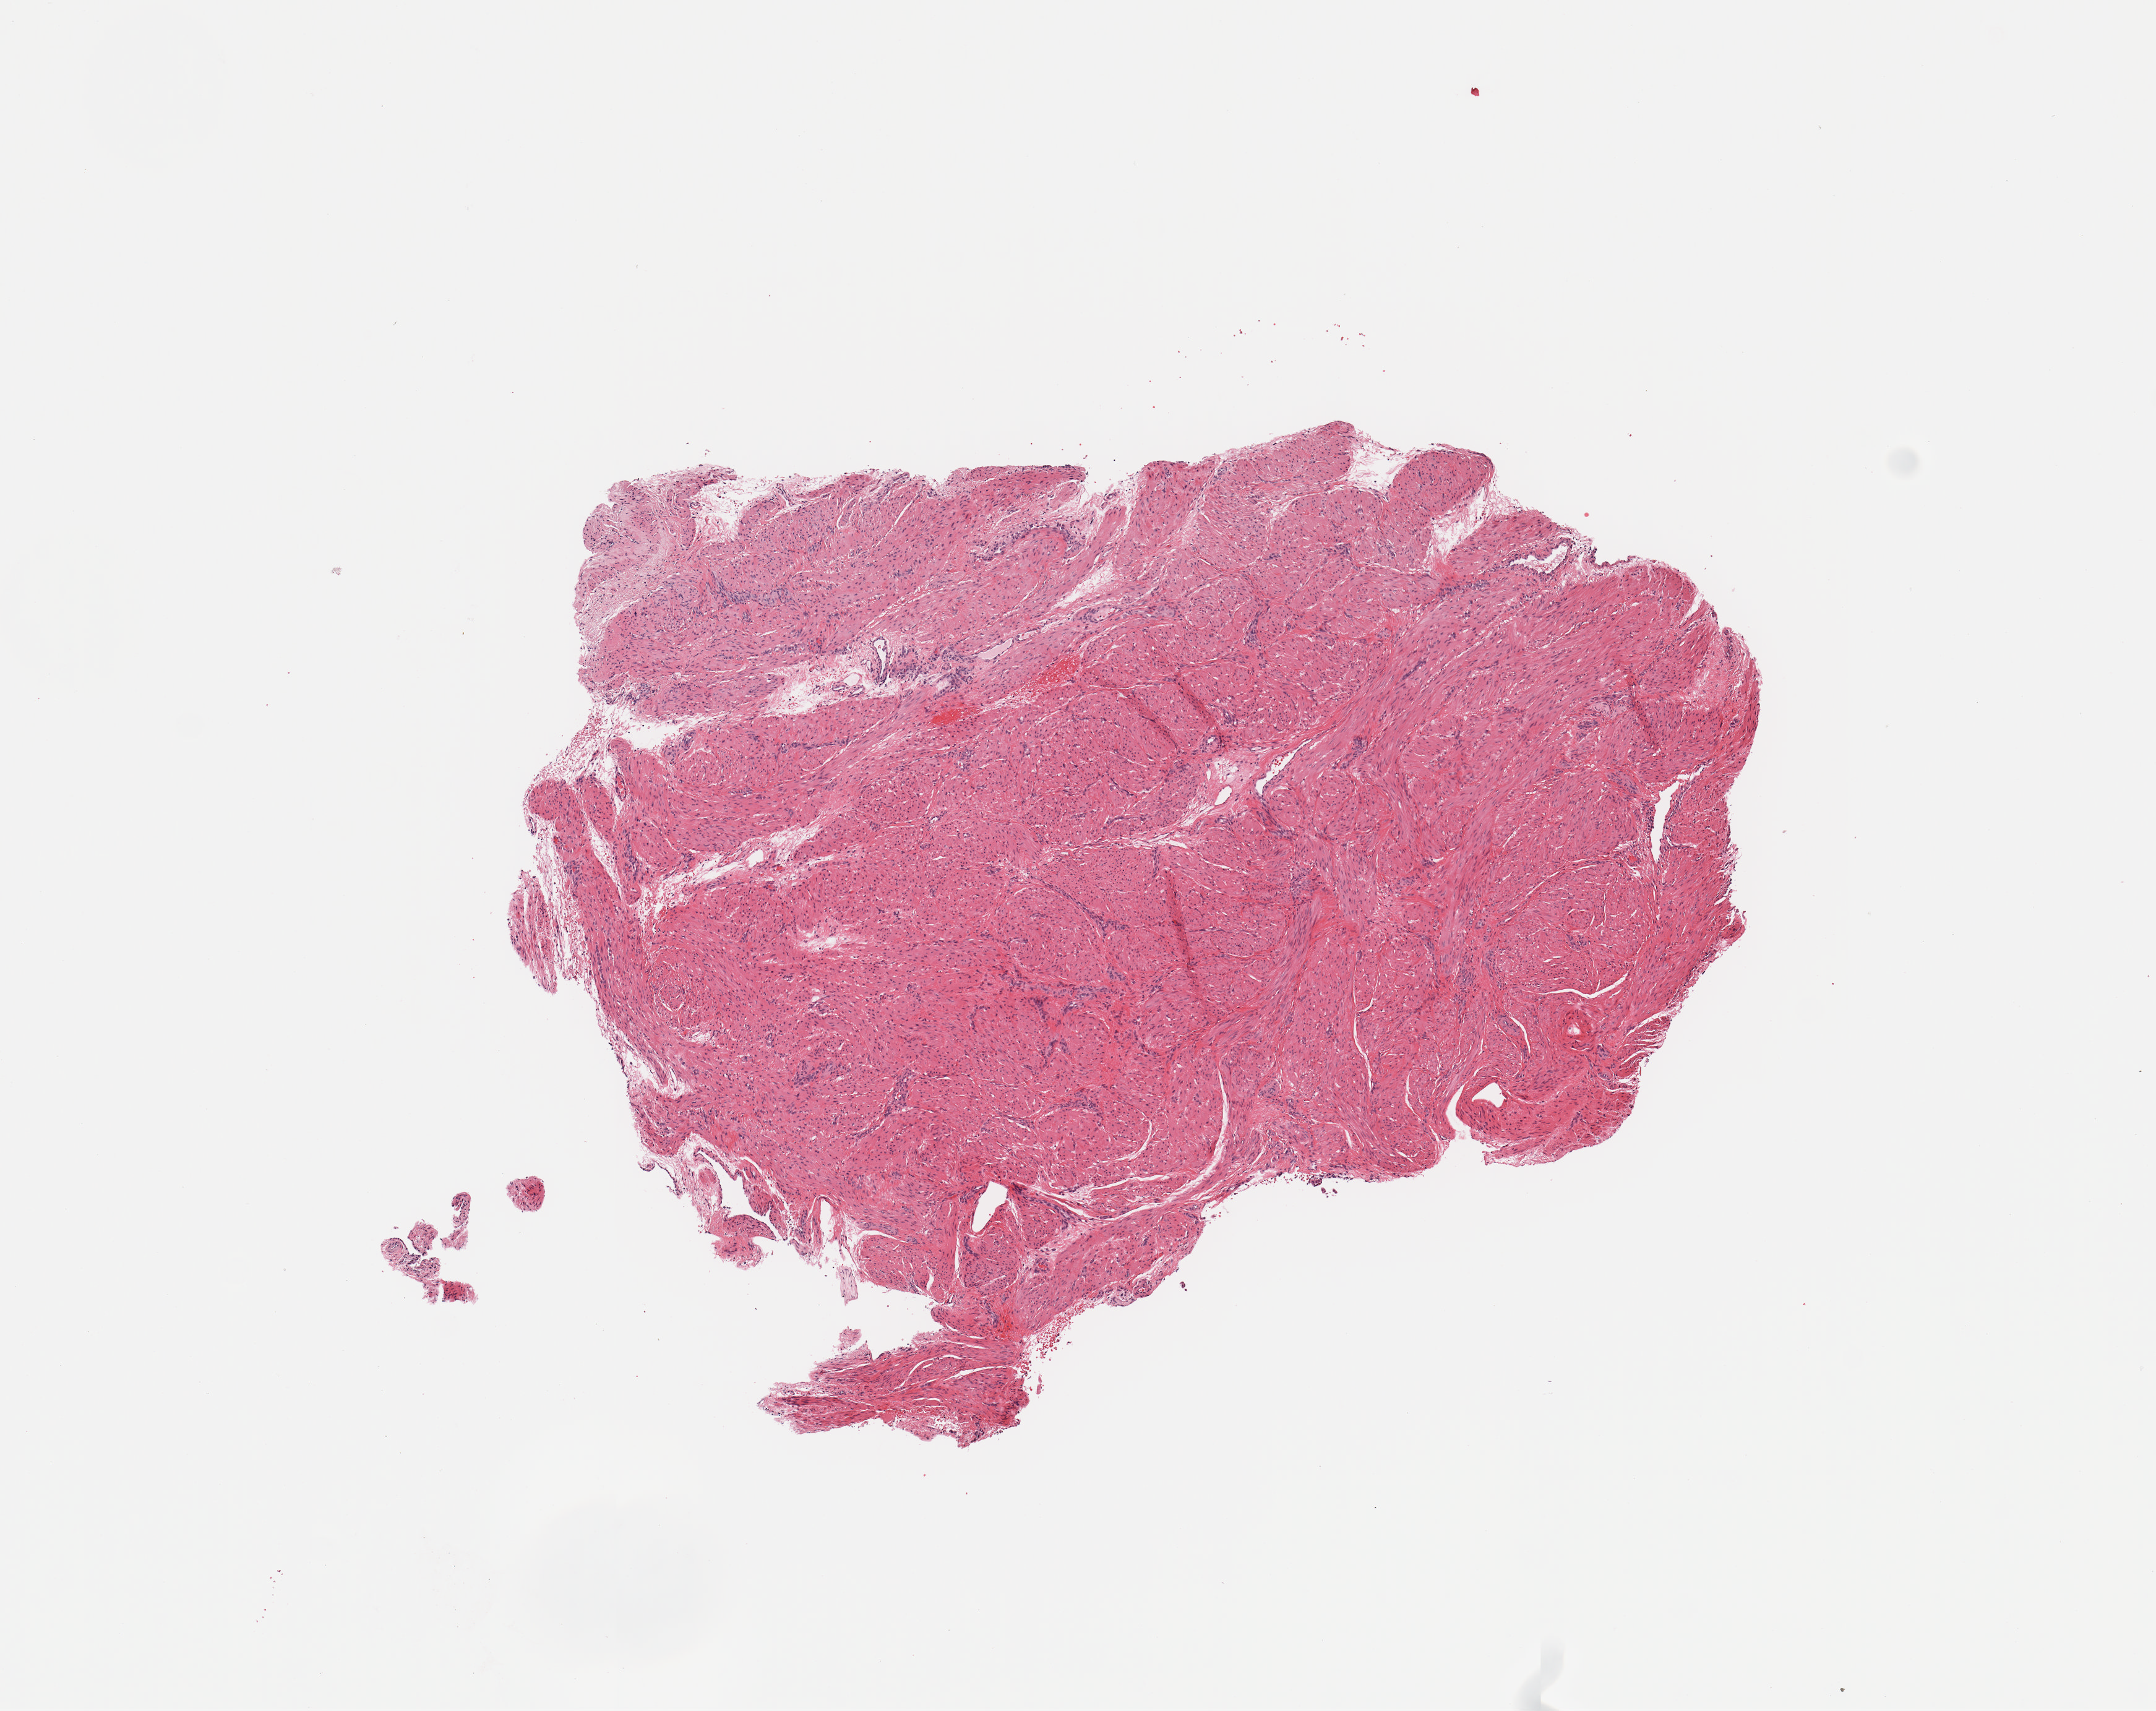
Digitized H&E-stained tissue section (whole slide) — whole scanned area (about 6.9 x 5.5 mm, slide scanned at 20x) shown as a low-resolution overview, normal (non-tumour) tissue sample, uterus. Patient: female, age 53 years.
This section: normal (non-tumour) tissue from the same patient. Patient diagnosis: Endometrioid adenocarcinoma, NOS.